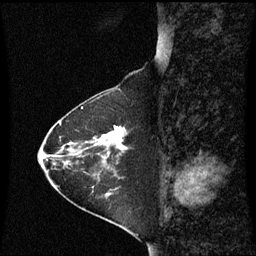
Breast MRI (dynamic contrast-enhanced), one sagittal slice. Dynamic contrast-enhanced series, image 2 of 3 at this slice position (ordered by acquisition). 1.5 T. TE 4.2 ms, TR 8.9 ms. 256 × 256 image matrix. Patient: female, 63 years. Case-level facts recorded for this patient, not image findings: setting: breast cancer imaged before/during neoadjuvant chemotherapy; receptor status: HR-positive, HER2-negative.
Structures marked on this image (semi-automatic segmentation, software-assisted and operator-edited):
- analysis volume of interest (the breast-tissue region the enhancement analysis was run in; not a lesion): bounding box [x1, y1, x2, y2] px = [88, 126, 128, 163]
- tumour enhancement mask (voxels above the 70 % enhancement threshold inside the analysis volume of interest): [100, 127, 125, 151]